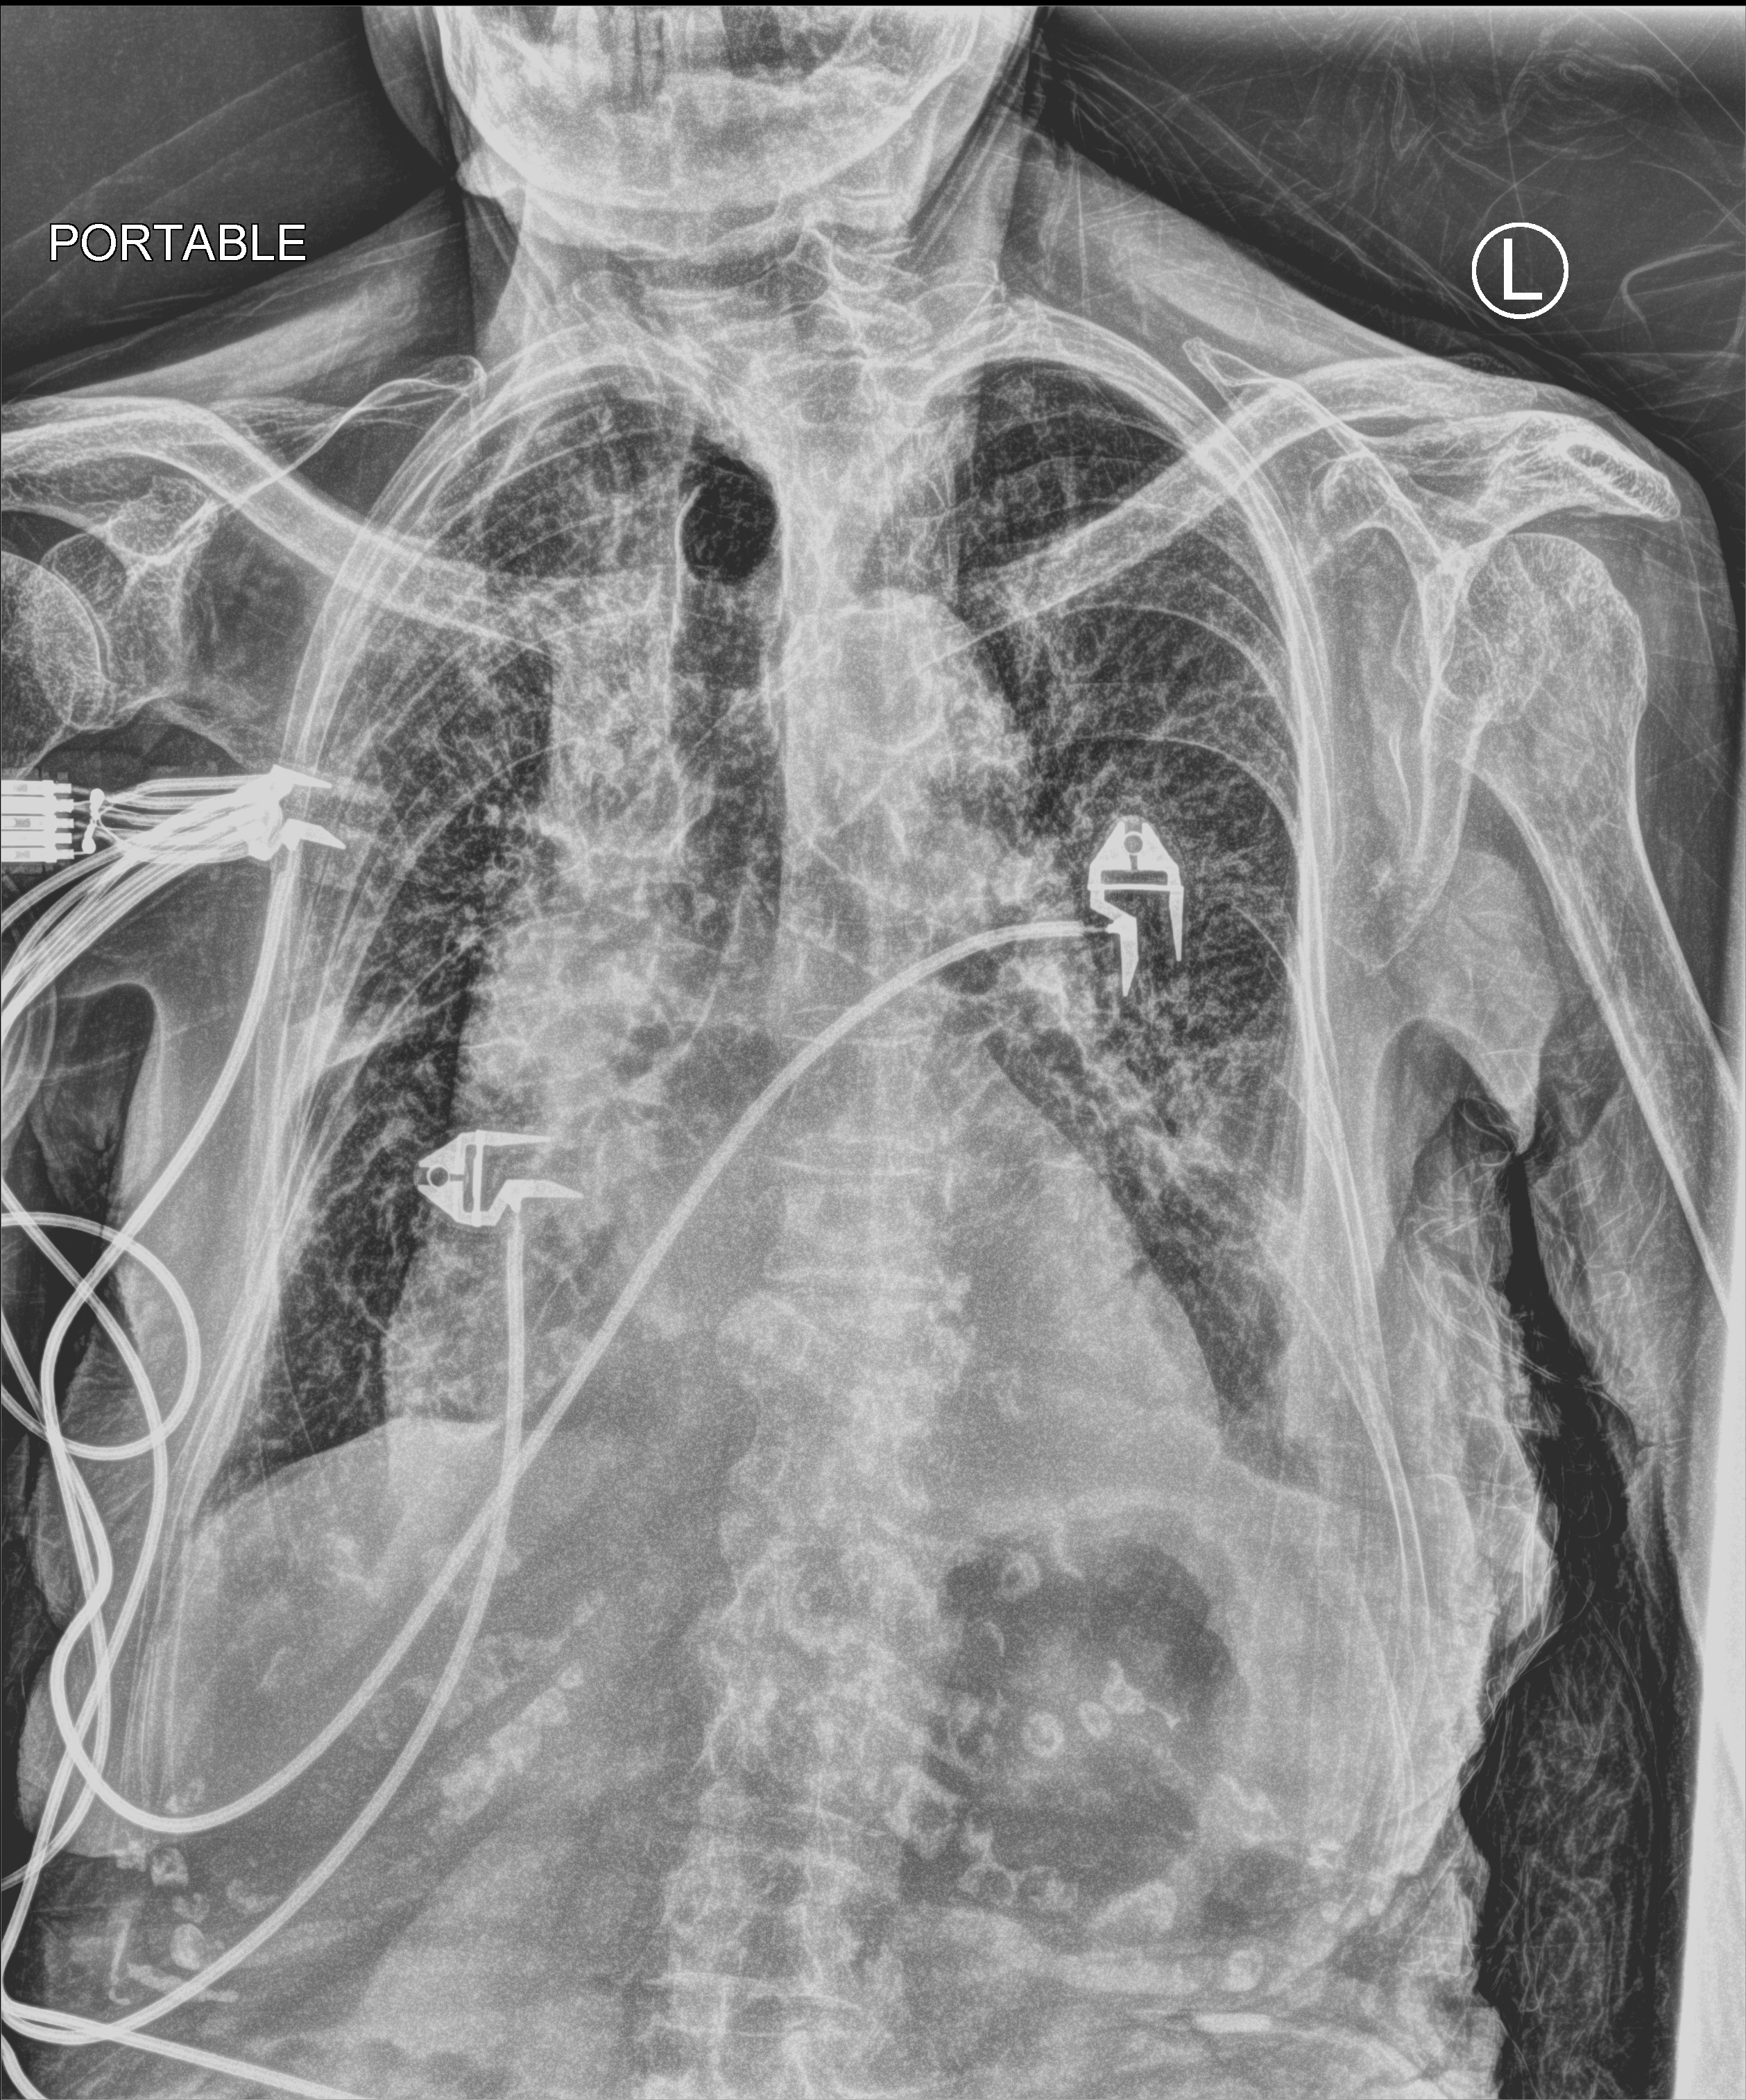
Portable chest radiograph; anteroposterior (AP) projection. Female patient hospitalised with COVID-19, age 75–90 years.
From the hospital-stay record, not from the radiograph (when in the stay this image was taken is not recorded):
- mechanically ventilated during this hospital stay: no